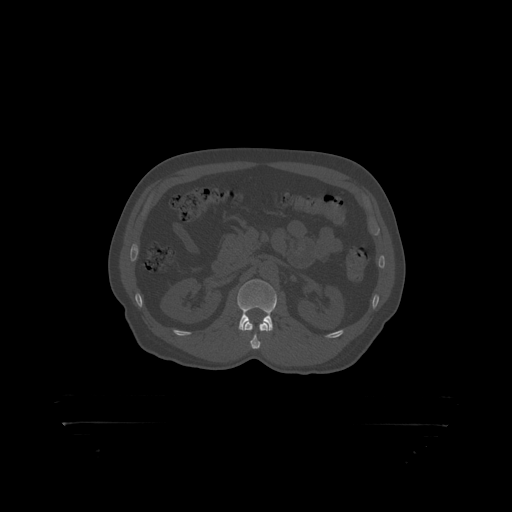
CT including the spine, one axial slice; slice 308 of 399 in the series (ordered by position); 120 kVp; bone window (W 1800 / L 400 HU); 1.25 mm slice thickness; 512 × 512 image matrix, field of view 650 × 650 mm. Patient: male, 46 years. From the clinical record (not read from this slice): primary cancer: skin.
Annotated regions visible in this slice (semi-automatic segmentation, software-assisted and operator-edited):
- L2 vertebra: bounding box <238,280,277,319> (left, top, right, bottom; pixels)